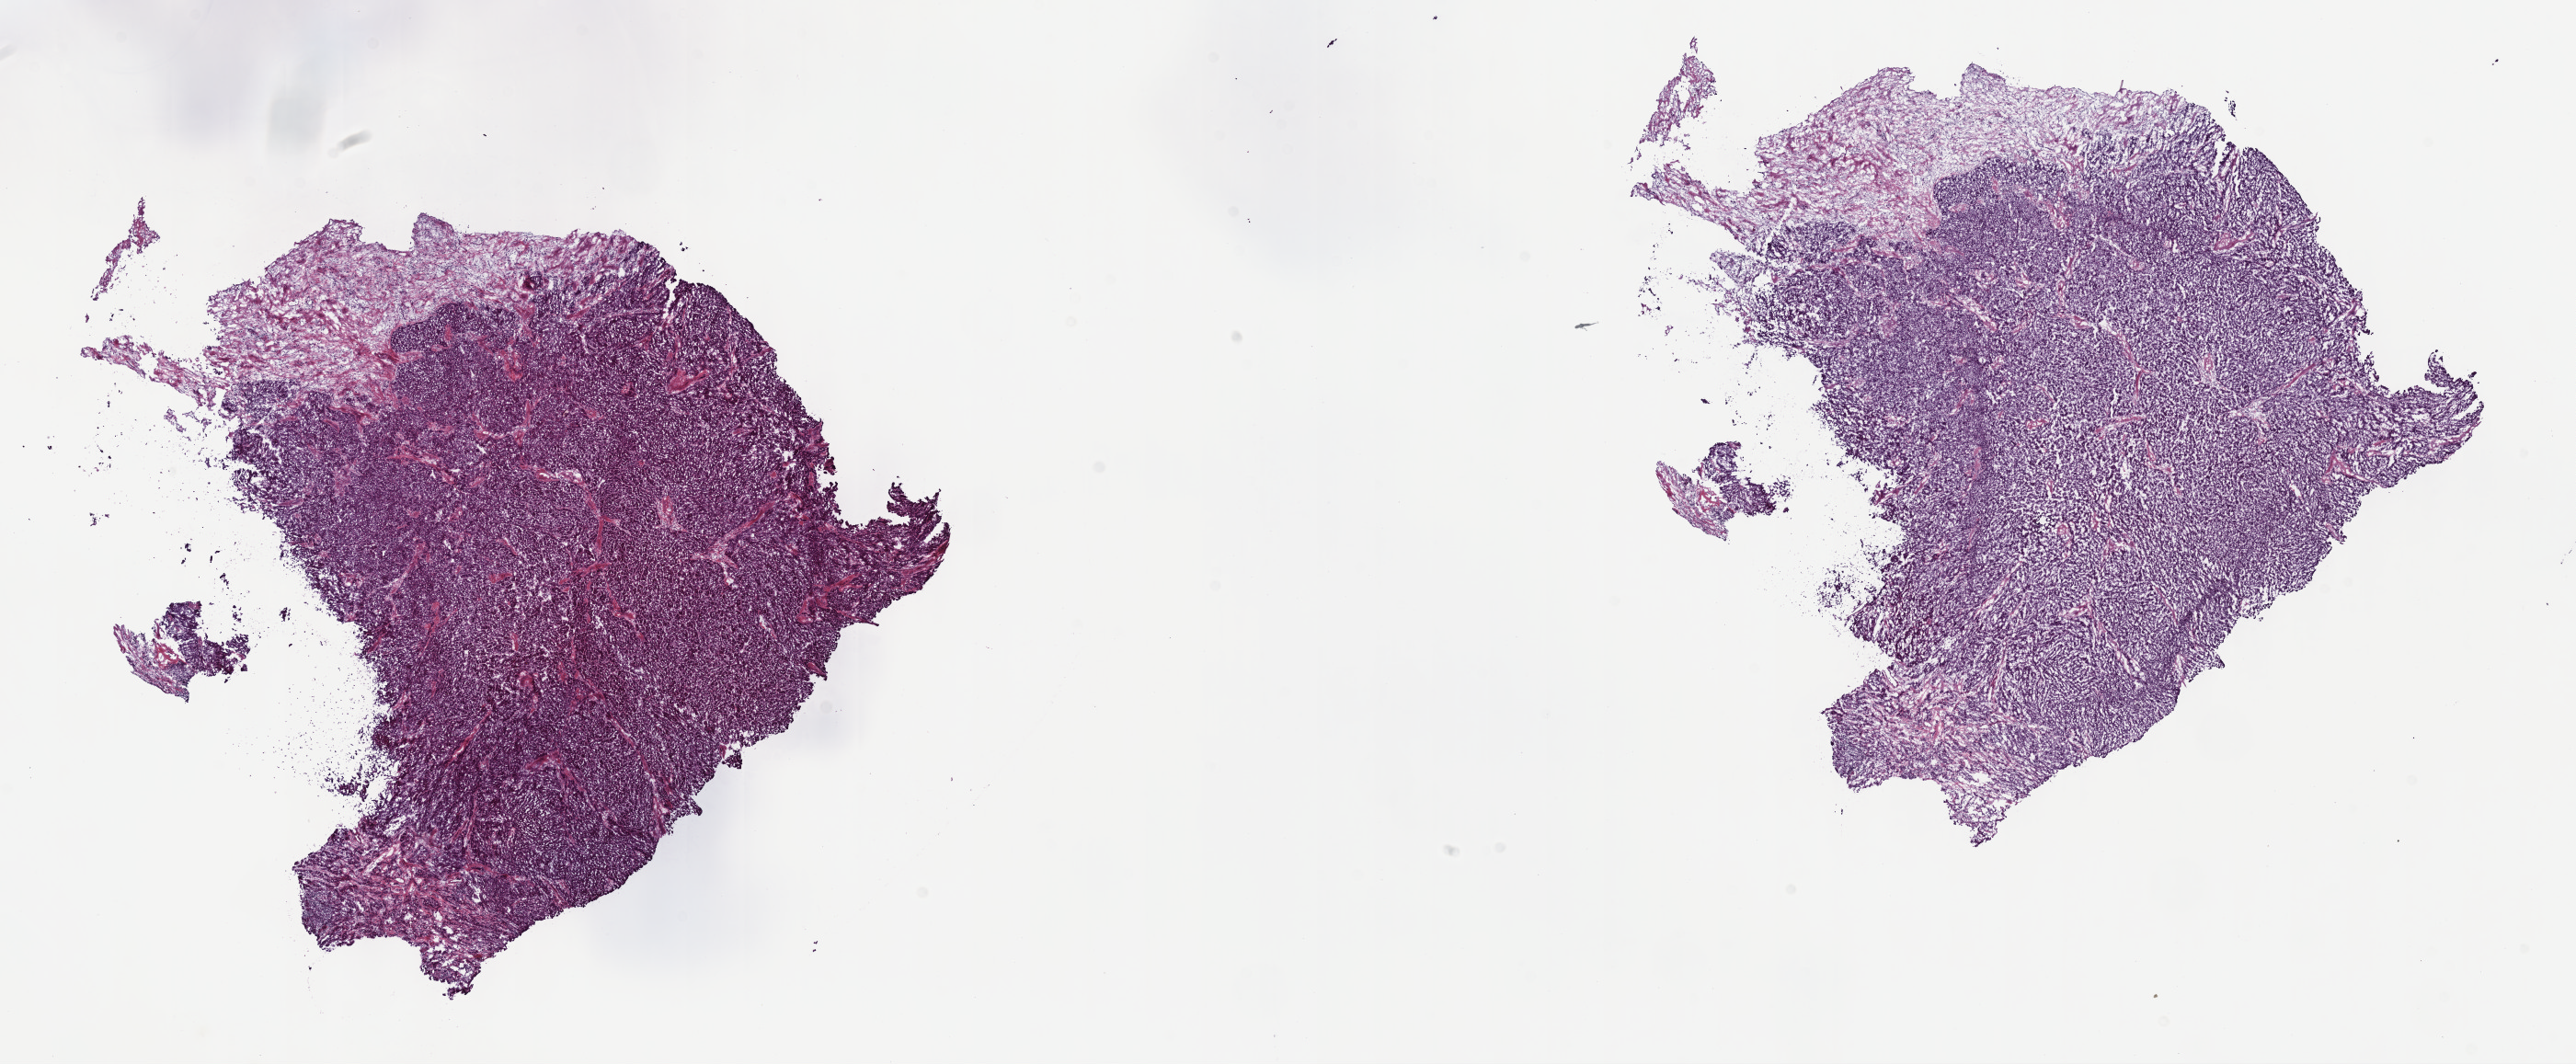
Whole-slide histology image, H&E-stained — shown as a low-resolution overview of the whole scanned area (about 22.7 x 9.4 mm, from a 40x scan). Frozen section from the top of the tissue portion. Sample: primary tumour, liver. Patient: male, age at initial diagnosis 66 years. Histologic grade: G2 (moderately differentiated). Slide review estimates, as recorded: tumour cells 90%, tumour nuclei 90%, normal cells 0%, stromal cells 8%, necrosis 2%. Infiltration values recorded for this section: lymphocyte infiltration 8%, monocyte infiltration 0%, neutrophil infiltration 1%.
TNM: T1 NX MX. AJCC pathologic stage: I (7th edition). Pathologic diagnosis: Hepatocellular carcinoma, NOS.